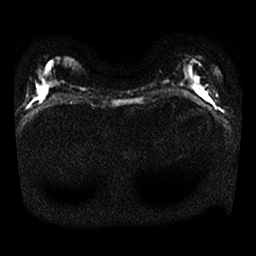
Breast MRI, one axial slice; position 9 of 25 along the scan axis; diffusion-weighted series; image 2 of 4 stored at this slice position (different b-values; order by instance number); 1.5 T; 4 mm slice thickness; 256 × 256 image matrix. Female patient.
Structures marked on this image (manually delineated by an expert):
- tumour on diffusion-weighted imaging: bounding box <204,94,211,102> (left, top, right, bottom; pixels)